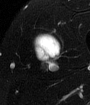
MRI of an extremity soft-tissue mass, one axial slice; slice 47 of 65 in the series (ordered by position); T2-weighted fat-saturated; MR volume resampled by the dataset authors to the PET/CT grid (not the native acquisition matrix); 90 × 105 image matrix, field of view 88 × 103 mm. Male patient. Case-level facts recorded for this patient, not image findings: histological type: mixoid liposarcoma; grade: low; site of the primary tumour: left thigh.
Structures marked on this image (expert contour drawn on MRI and transferred to this co-registered scan by the dataset authors):
- gross tumour volume (mass): bounding box <32,36,58,63> (left, top, right, bottom; pixels)